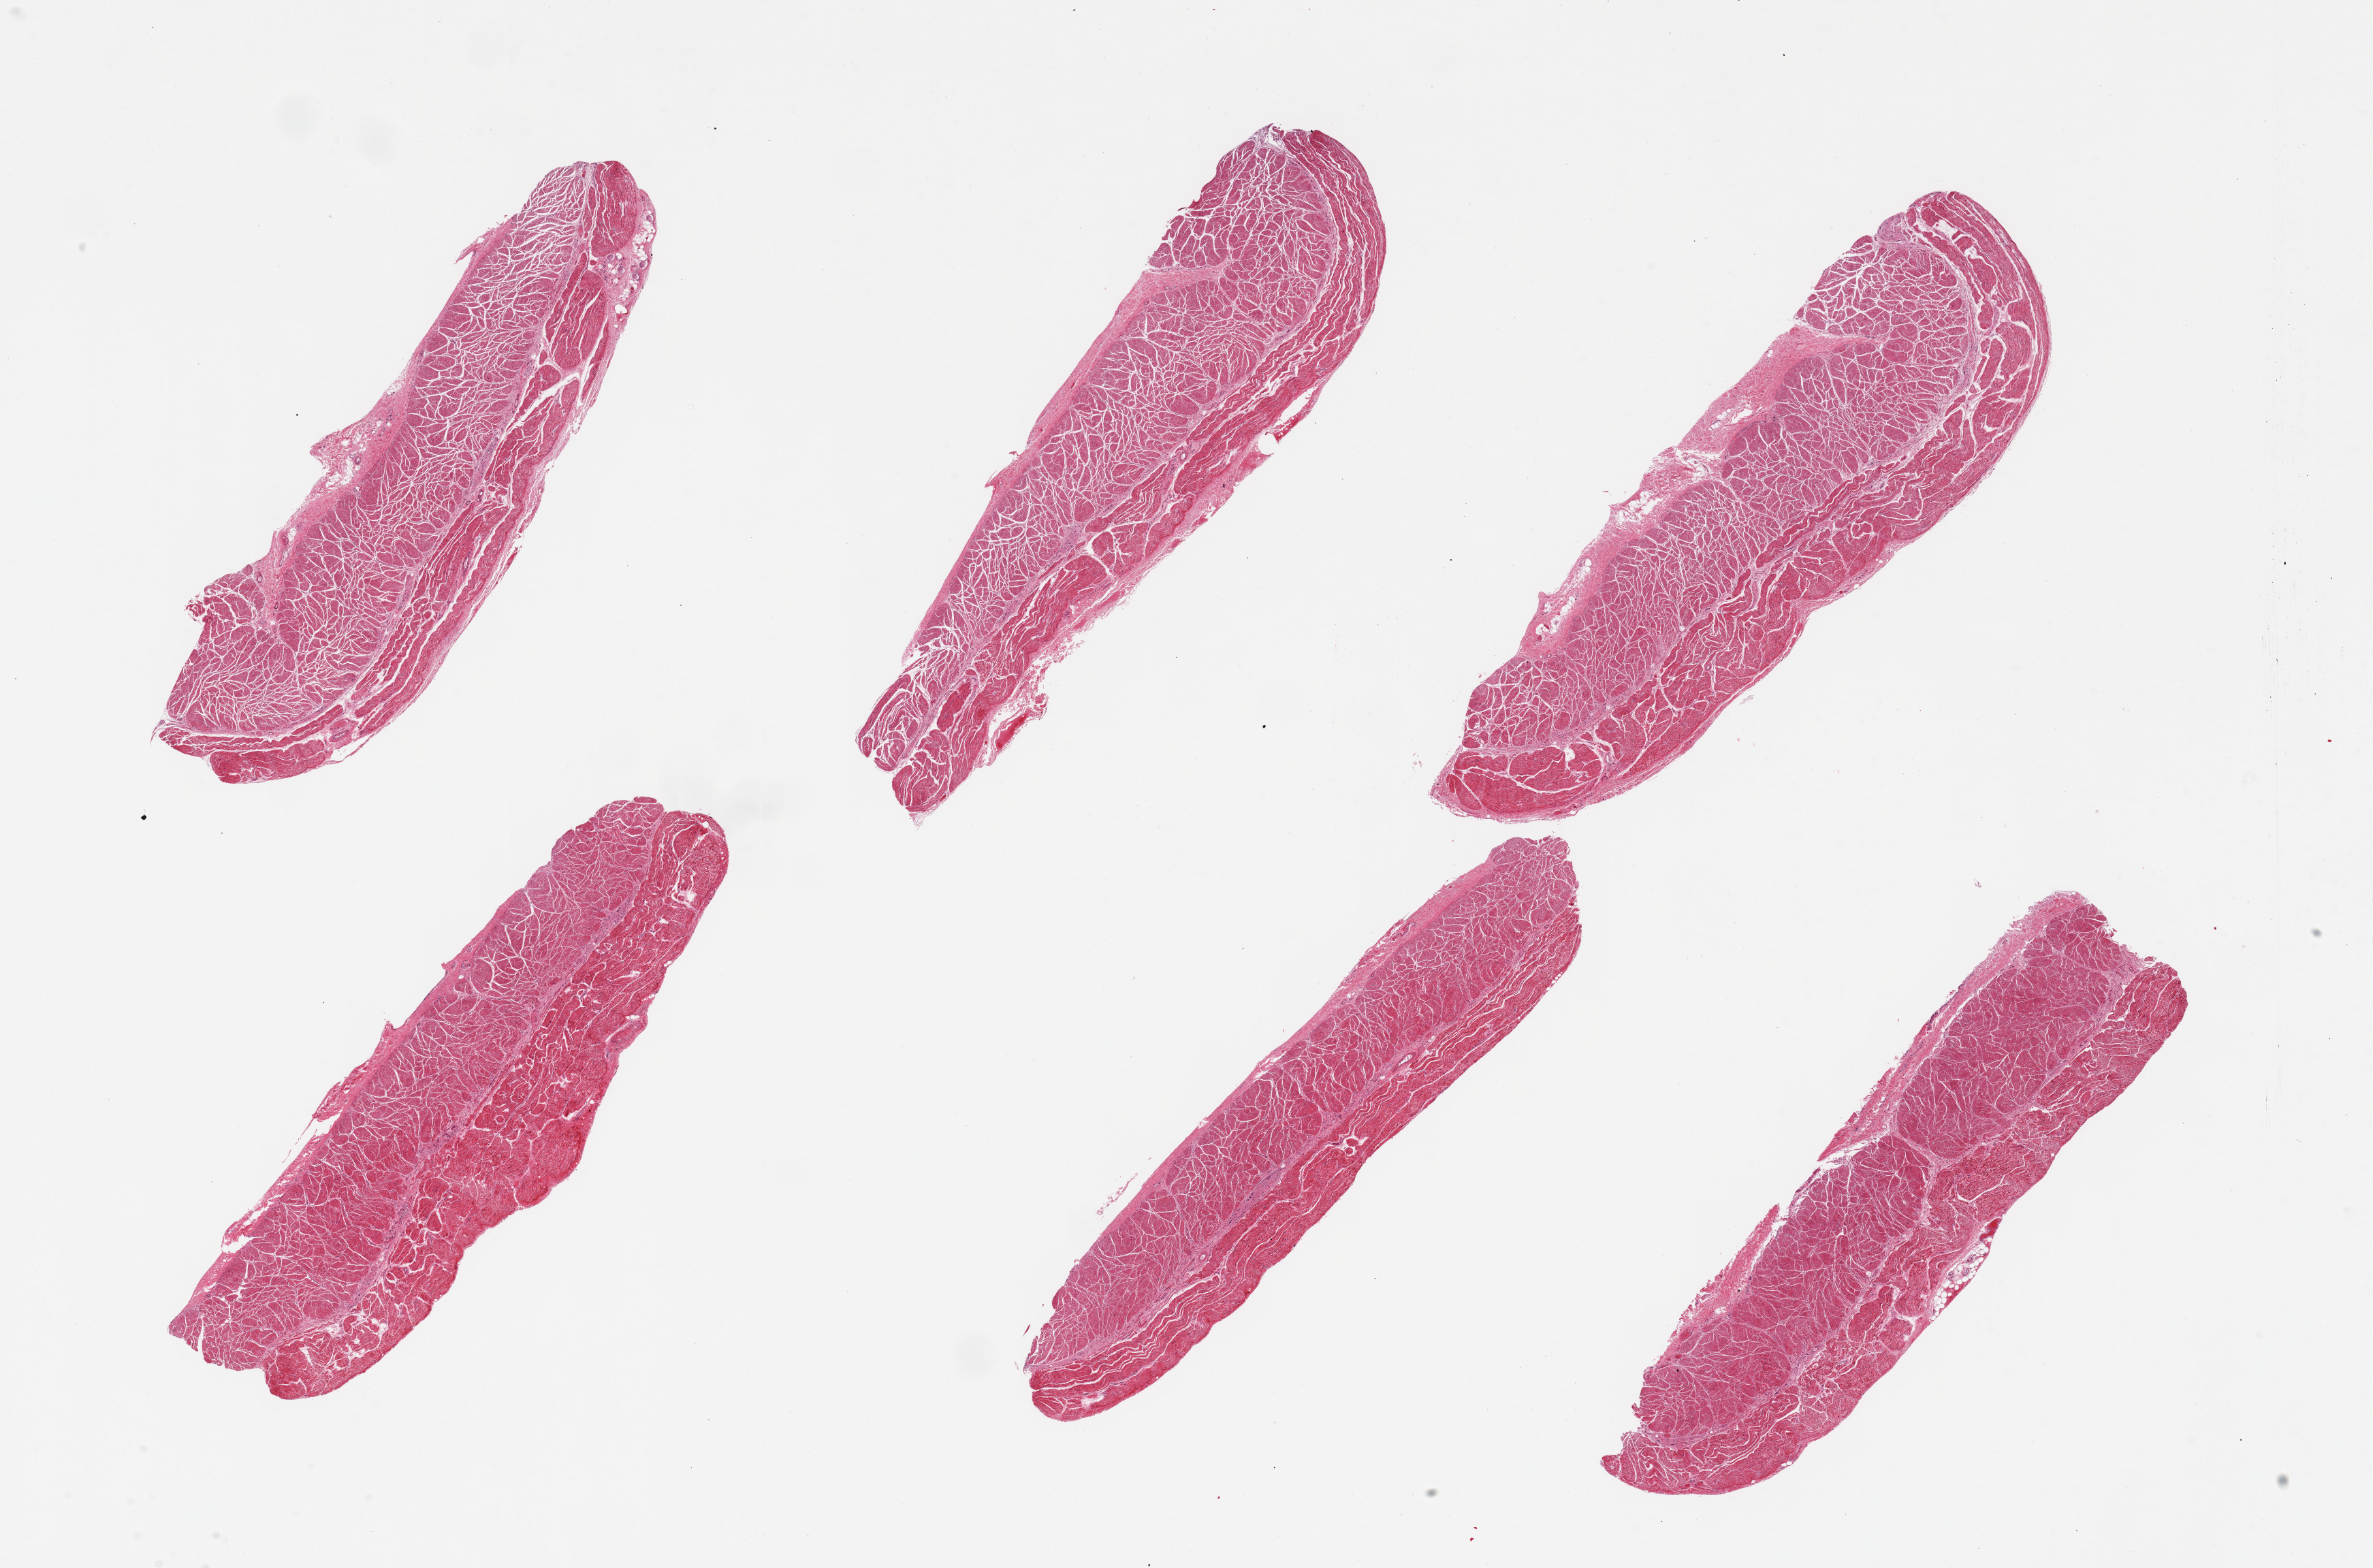
Digitized hematoxylin and eosin (H&E)-stained section, whole scanned area (about 27.6 x 18.2 mm, acquisition: 20x scan) shown as a low-resolution overview; PAXgene-fixed, paraffin-embedded tissue; sampled site (target tissue): esophageal muscle; tissue donor sample. Donor: male.
Pathologist's review note for this sample: 6 pieces; well trimmed target muscularis.